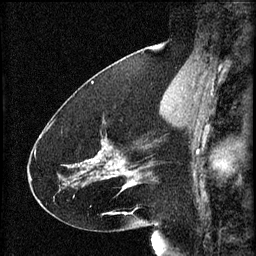
Breast MRI (dynamic contrast-enhanced), one sagittal slice. Position 27 of 60 along the scan axis. 3 images stored at this slice position (order not interpretable as contrast timing). 1.5 T. TE 4.2 ms, TR 8.2 ms. 2 mm slice thickness. 256 × 256 image matrix, field of view 180 × 180 mm. Patient: female, 41 years.
Outlined on this slice (semi-automatically segmented with operator editing):
- analysis volume of interest (the breast-tissue region the enhancement analysis was run in; not a lesion): box from (x=72, y=120) to (x=134, y=195) px
- tumour enhancement mask (voxels above the 70 % enhancement threshold inside the analysis volume of interest): (x=75, y=148)–(x=134, y=189)